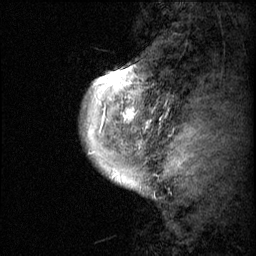
Breast MRI (dynamic contrast-enhanced), one sagittal slice. Position 7 of 60 along the scan axis. Dynamic contrast-enhanced series, image 2 of 3 at this slice position (ordered by acquisition). 1.5 T. TE 4.2 ms, TR 11.1 ms. 2 mm slice thickness. 256 × 256 image matrix, field of view 180 × 180 mm. Female patient, age 50 years.
Outlined on this slice (semi-automatically segmented with operator editing):
- analysis volume of interest (the breast-tissue region the enhancement analysis was run in; not a lesion): box from (x=82, y=60) to (x=160, y=143) px
- tumour enhancement mask (voxels above the 70 % enhancement threshold inside the analysis volume of interest): (x=92, y=64)–(x=147, y=143)